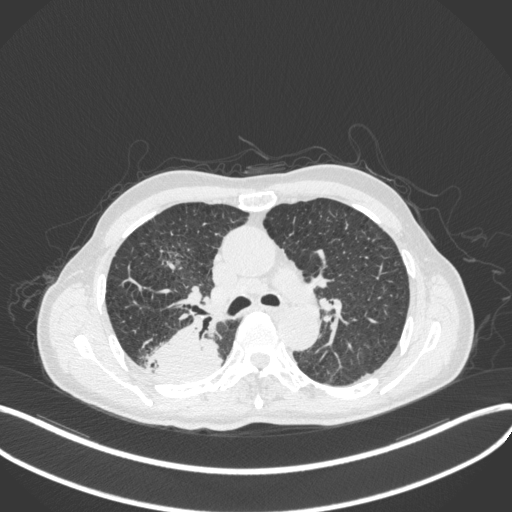
Chest CT, one axial slice. Position 294 of 423 along the scan axis. Lung window (W 1500 / L -600 HU). 1 mm slice thickness. 512 × 512 image matrix, field of view 400 × 400 mm. Patient: male, 79 years. Case-level facts recorded for this patient, not image findings: clinical TNM (as recorded): T3 N0 M0.
Structures marked on this image (rectangle marked by the reading radiologist):
- lung tumour (recorded histology: adenocarcinoma): bounding box <142,323,224,383> (left, top, right, bottom; pixels)